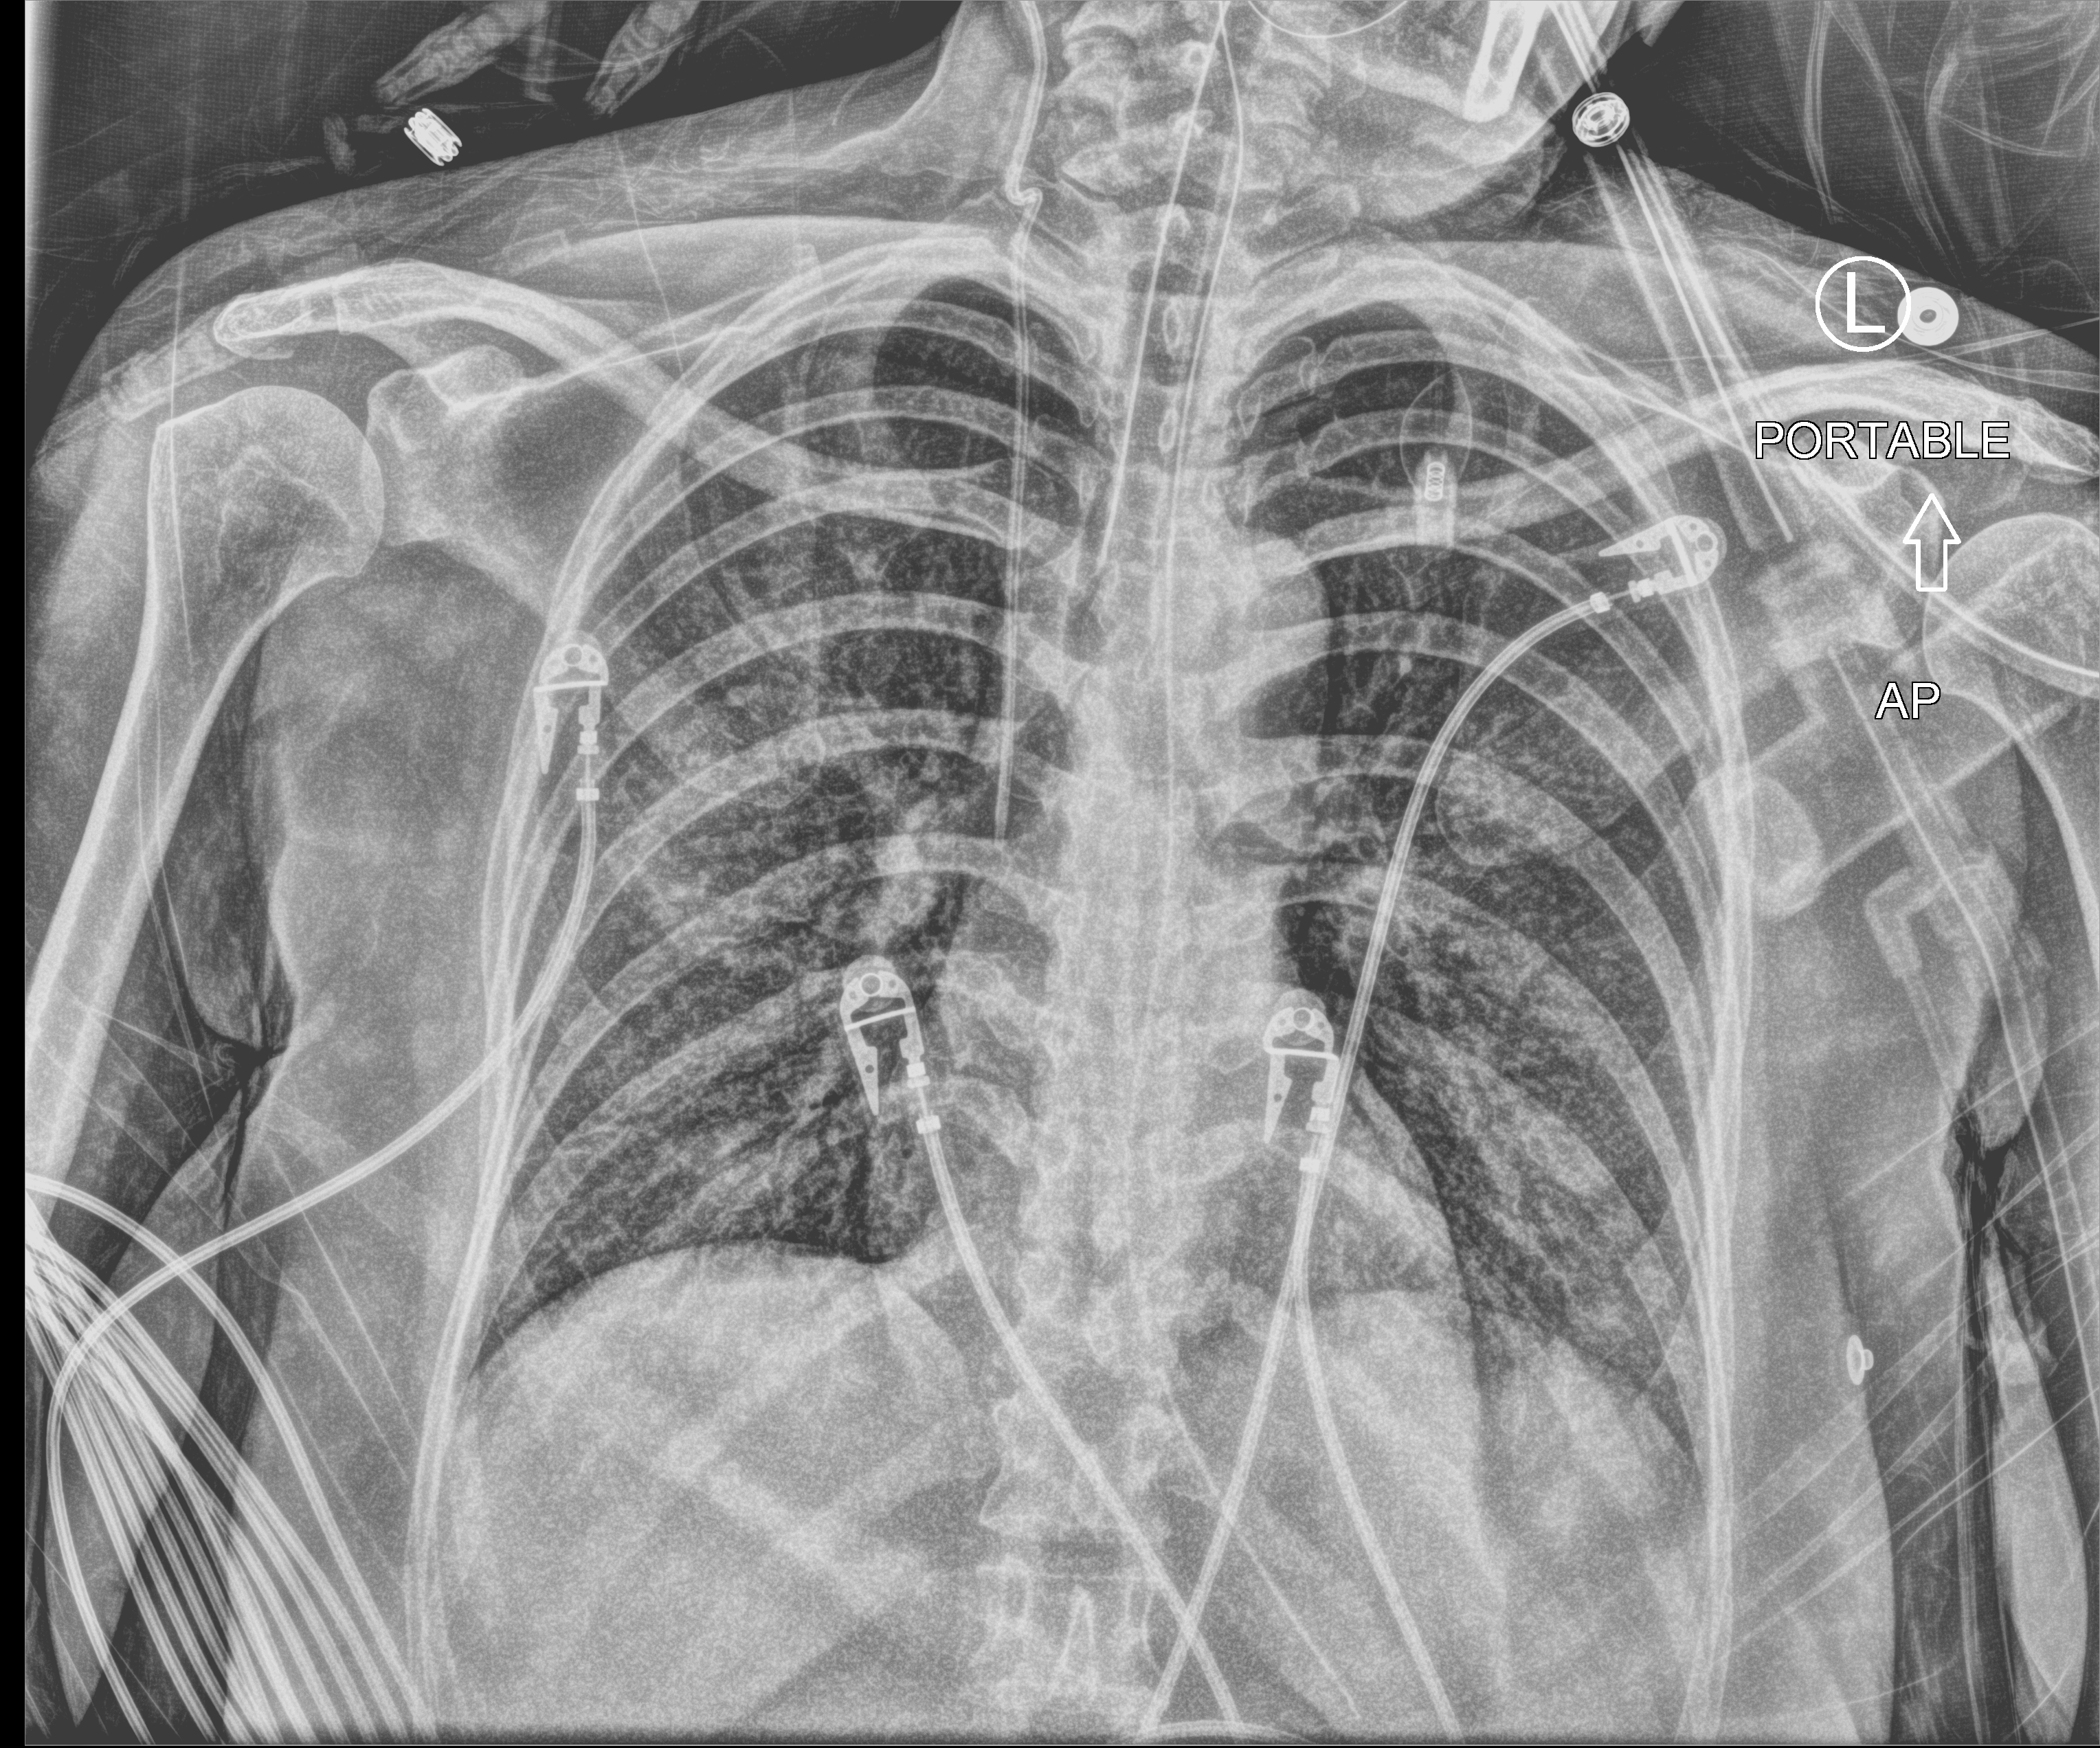
Bedside chest radiograph (computed radiography); anteroposterior (AP) projection. Female patient hospitalised with COVID-19, age 18–59 years.
Admission-level facts for this patient (not findings on this image; timing relative to this image not recorded):
- admitted to intensive care during this hospital stay: yes
- mechanically ventilated during this hospital stay: yes
- hypertension (admission record): yes